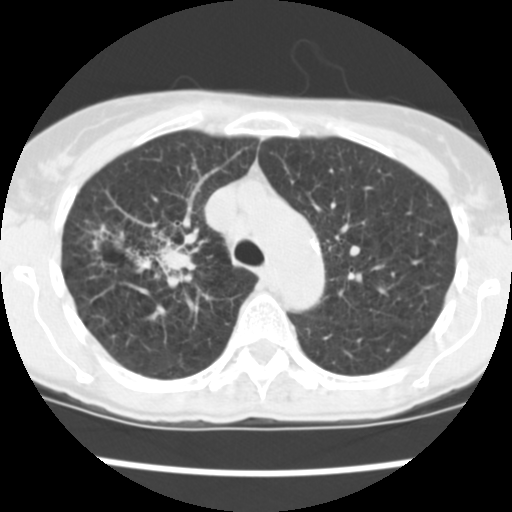
Low-dose screening chest CT, axial slice. Baseline annual screen. Lung window (W 1500 / L -600 HU). 2.5 mm slice thickness. Standard (soft-tissue) reconstruction kernel (STANDARD). 120 kVp. Slice 178 of 252 in the series. Female, age 60 years at enrolment. Current smoker at enrolment.
Expert-annotated lung lesion, bounding box (x1, y1, x2, y2) in pixels: (84, 216, 200, 286). The screening reader recorded 3 non-calcified nodules or masses ≥4 mm on this exam; which of them this box marks is not recorded. Later outcome: lung cancer diagnosed 19 days after this screen — non-small cell carcinoma, right upper lobe, stage IV (AJCC 6th edition), 26 mm at pathology.